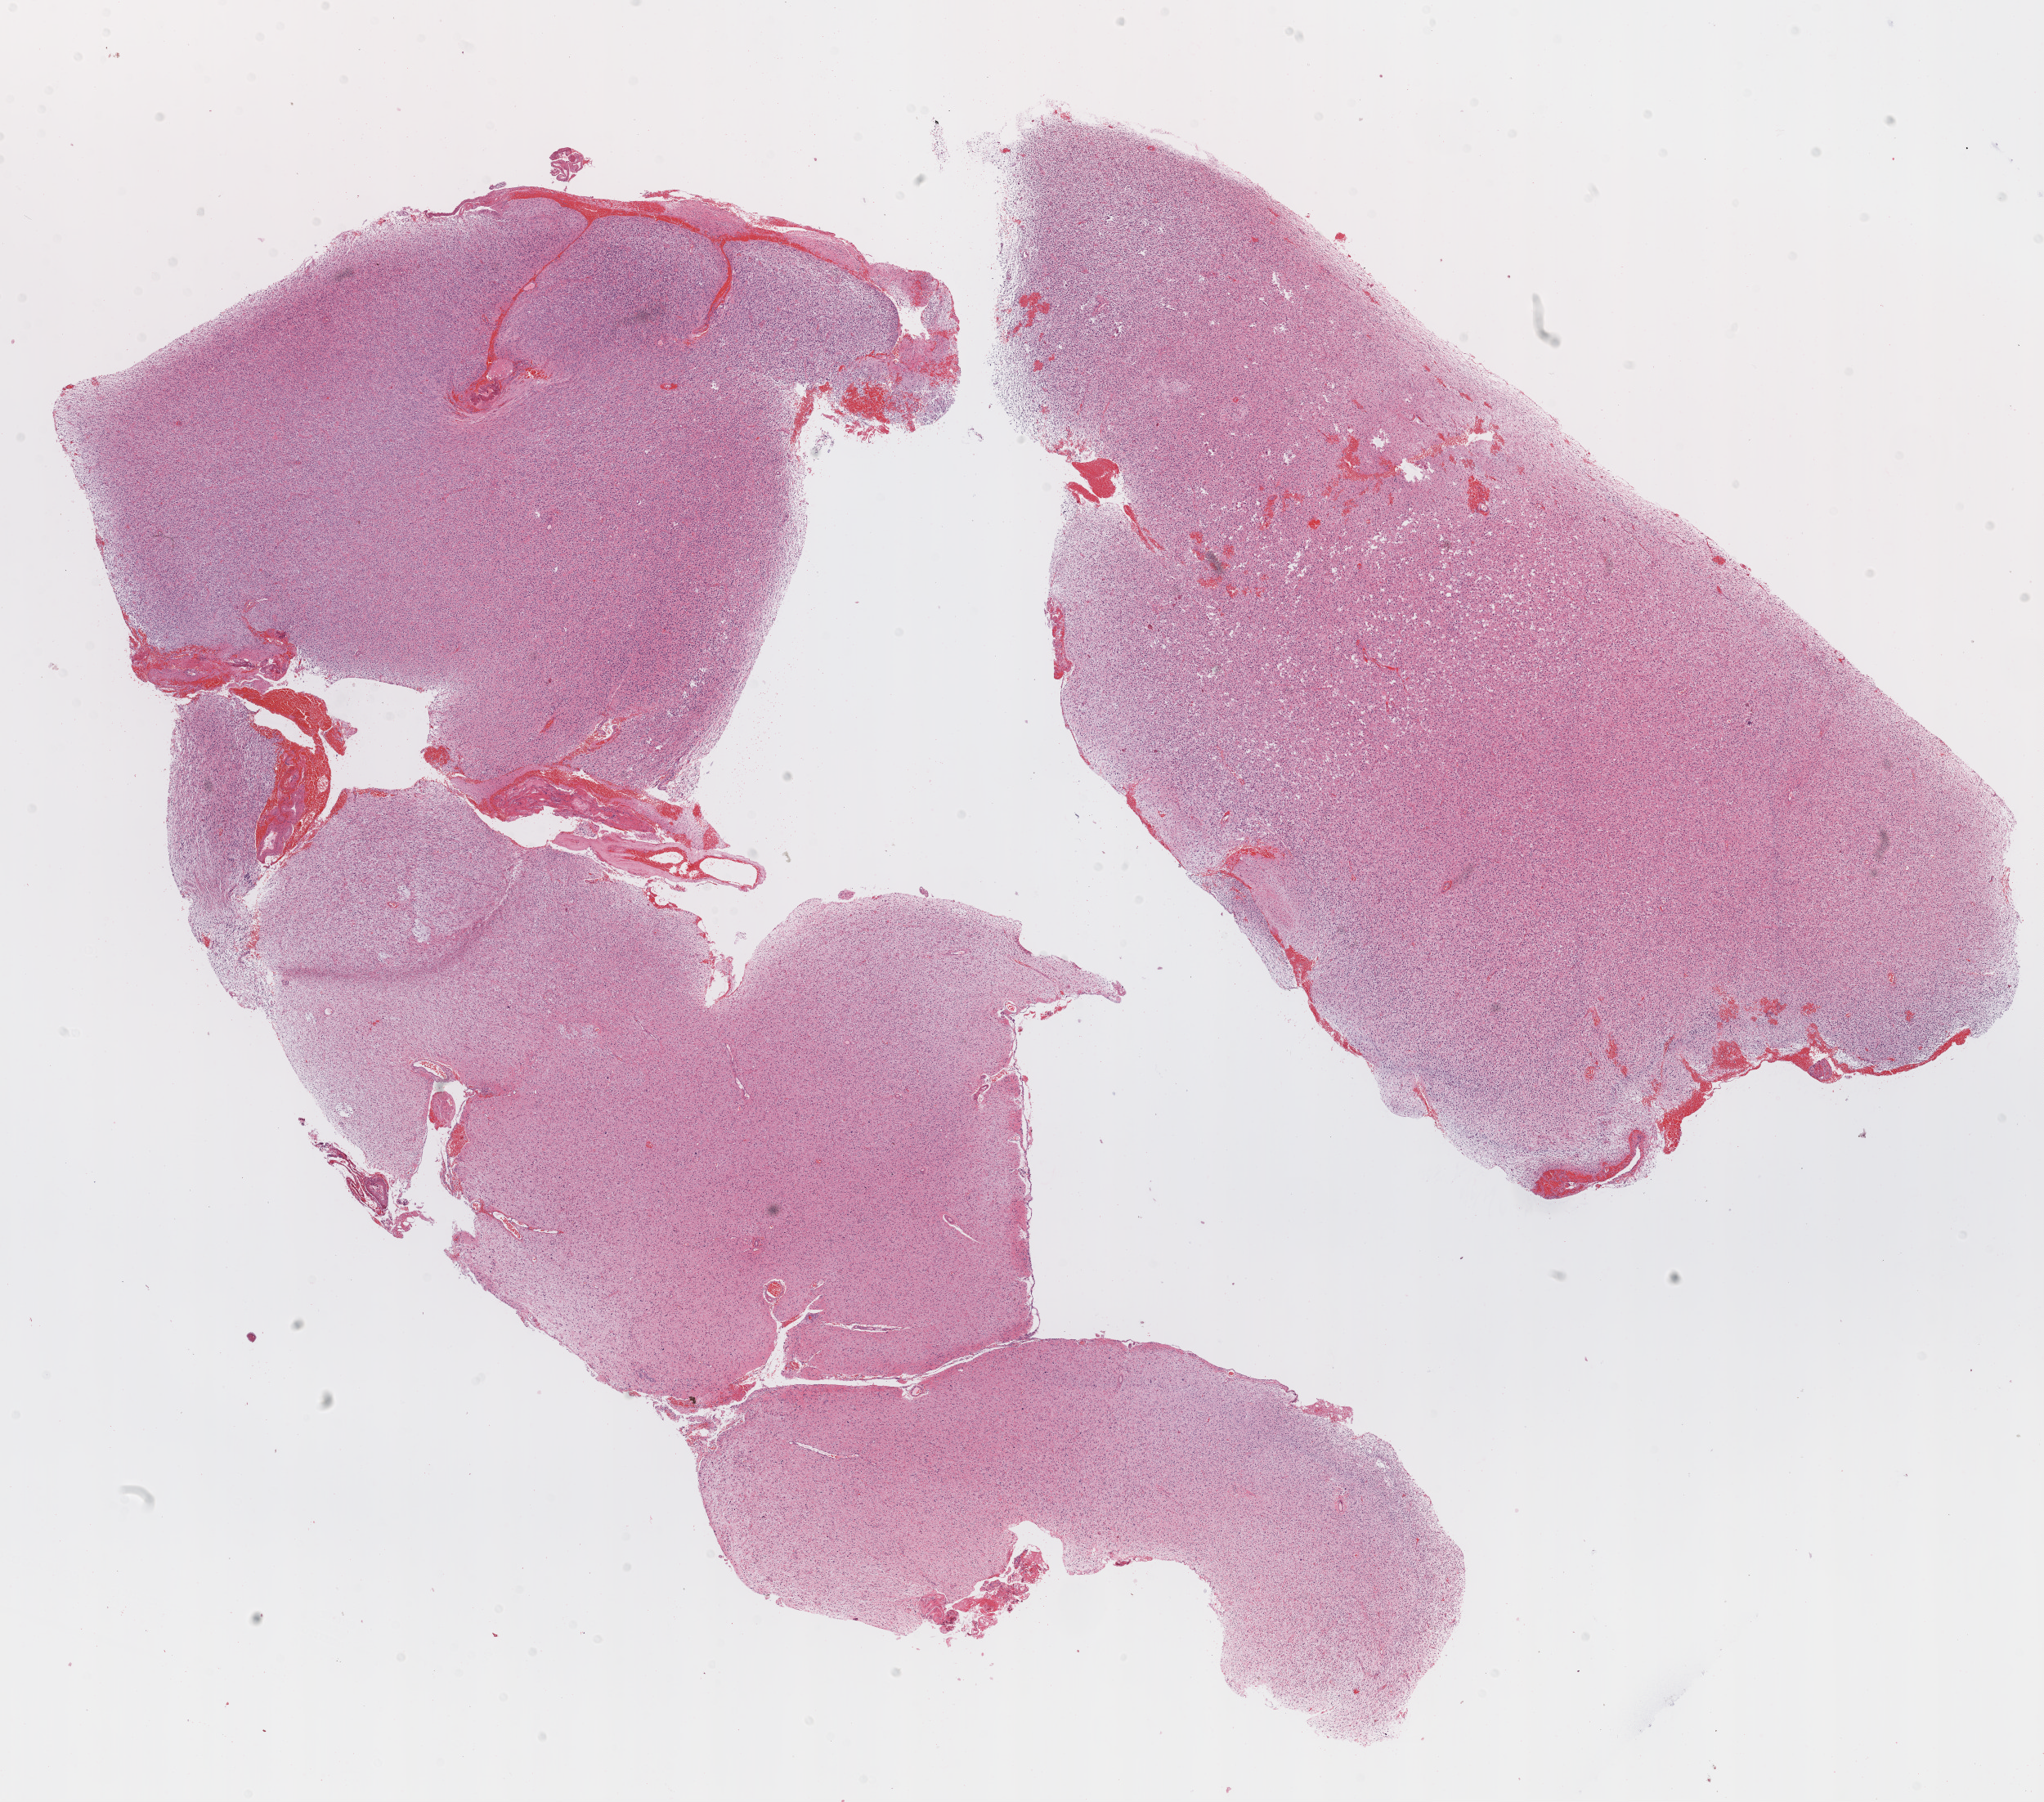
Digitized H&E tissue section (whole slide), low-resolution overview of the scanned area, about 20.1 x 17.7 mm (acquisition: 20x scan), formalin-fixed paraffin-embedded (FFPE) diagnostic section, brain, primary tumour sample. Patient: male, age at initial diagnosis 38 years.
• pathologic diagnosis: Glioblastoma